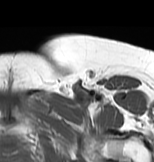
MRI of an extremity soft-tissue mass, one axial slice. Slice 57 of 83 in the series (ordered by position). MR volume resampled by the dataset authors to the PET/CT grid (not the native acquisition matrix). 3.27 mm slice thickness. 154 × 162 image matrix, field of view 150 × 158 mm. Female patient. Case-level facts recorded for this patient, not image findings: histological type: myxofibrosarcoma; grade: intermediate; site of the primary tumour: left thigh.
Outlined on this slice (expert contour drawn on MRI and transferred to this co-registered scan by the dataset authors):
- gross tumour volume including surrounding oedema: bounding box <44,89,114,115> (left, top, right, bottom; pixels)